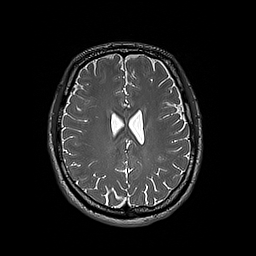
Brain MRI from a brain-tumour surgery series, one axial slice. Position 73 of 192 along the scan axis. 1 mm slice thickness. 256 × 256 image matrix. From the clinical record (not read from this slice): histopathology: Oligodendroglioma; WHO grade: 3; IDH mutation: yes; tumour location: Left Frontal.
Structures marked on this image (expert manual segmentation):
- tumour: bounding box [x1, y1, x2, y2] px = [147, 123, 151, 125]